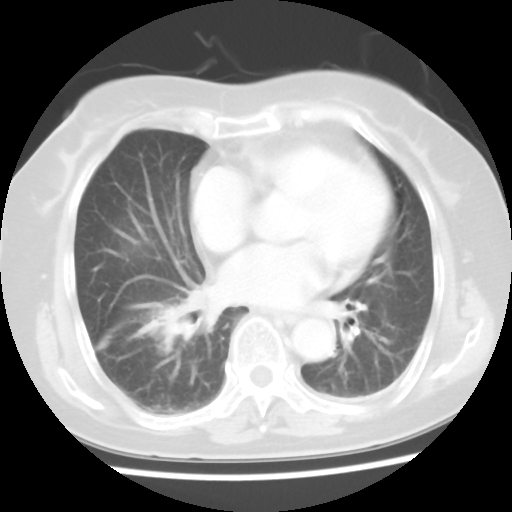
Chest CT, one axial slice. Position 18 of 45 along the scan axis. 120 kVp. Lung window (W 1500 / L -600 HU). 5 mm slice thickness. 512 × 512 image matrix, field of view 312 × 312 mm. Female patient, age 65 years. Case-level facts recorded for this patient, not image findings: clinical TNM (as recorded): T2 N3 M0.
Annotated regions visible in this slice (rectangle marked by the reading radiologist):
- lung tumour (recorded histology: adenocarcinoma): bounding box [x1, y1, x2, y2] px = [136, 299, 201, 359]